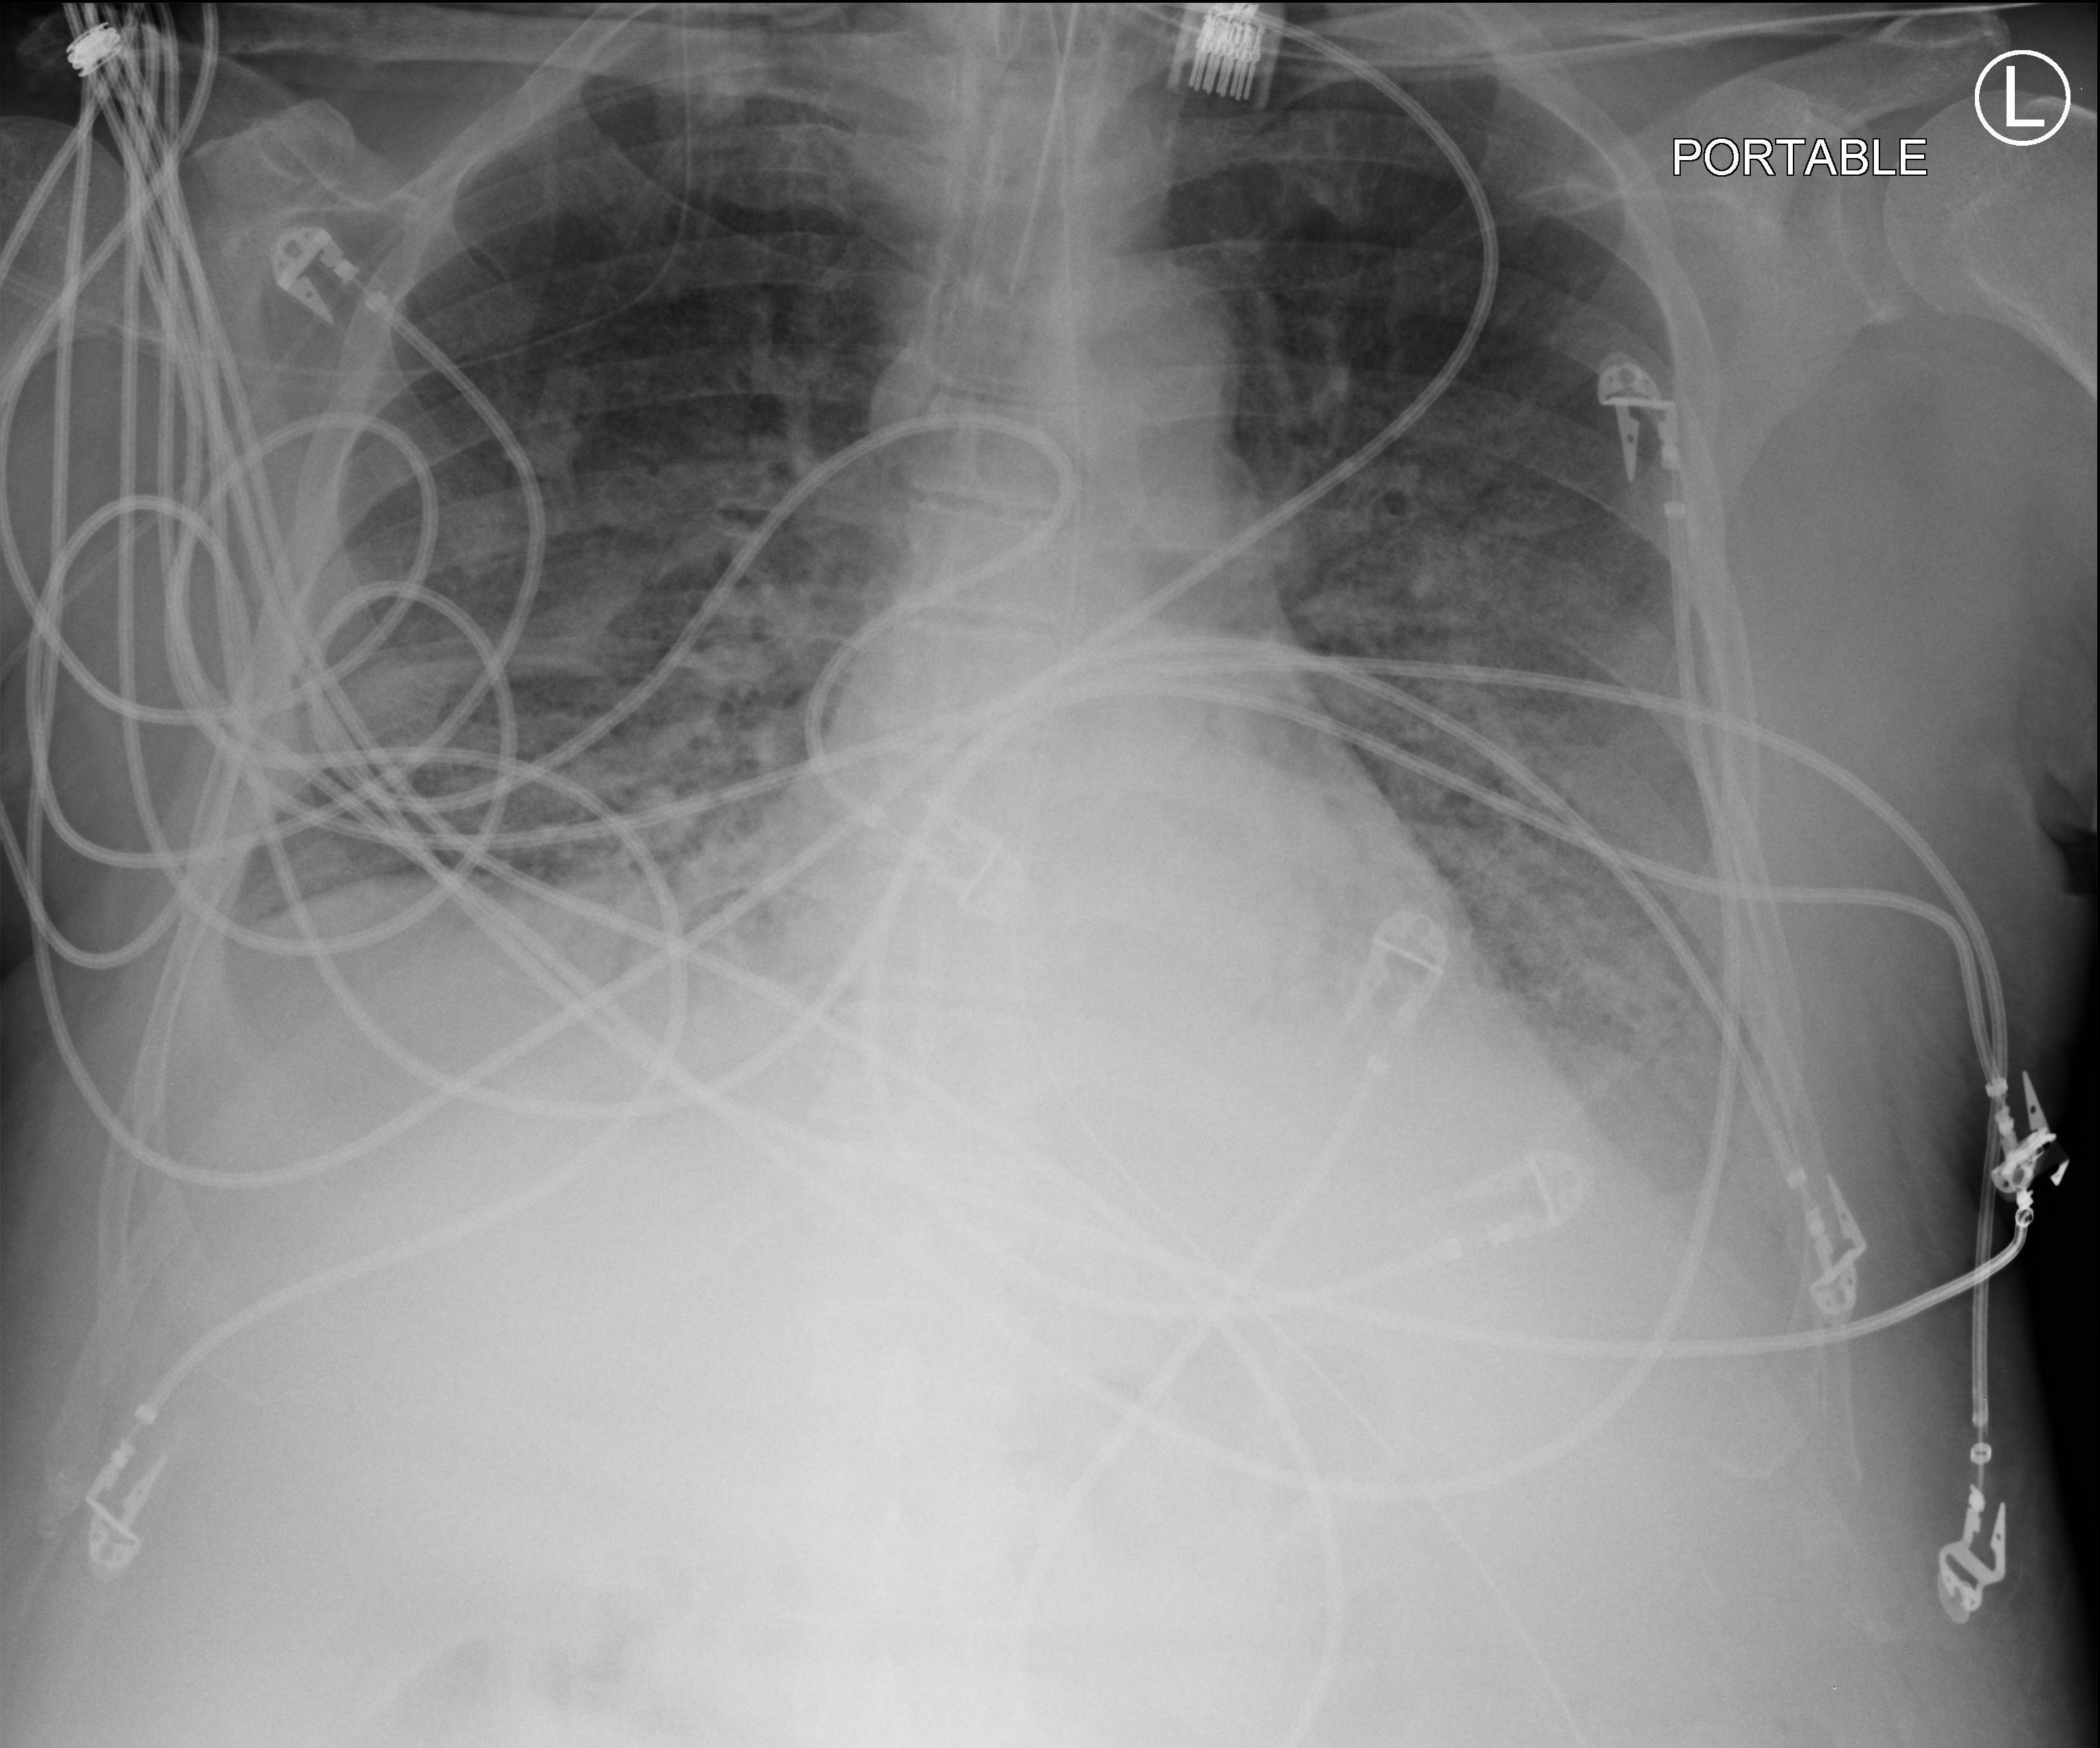
Bedside chest radiograph (computed radiography), anteroposterior (AP) projection. Male patient hospitalised with COVID-19, age 60–74 years.
Admission-level facts for this patient (not findings on this image; timing relative to this image not recorded): admitted to intensive care during this hospital stay: yes.